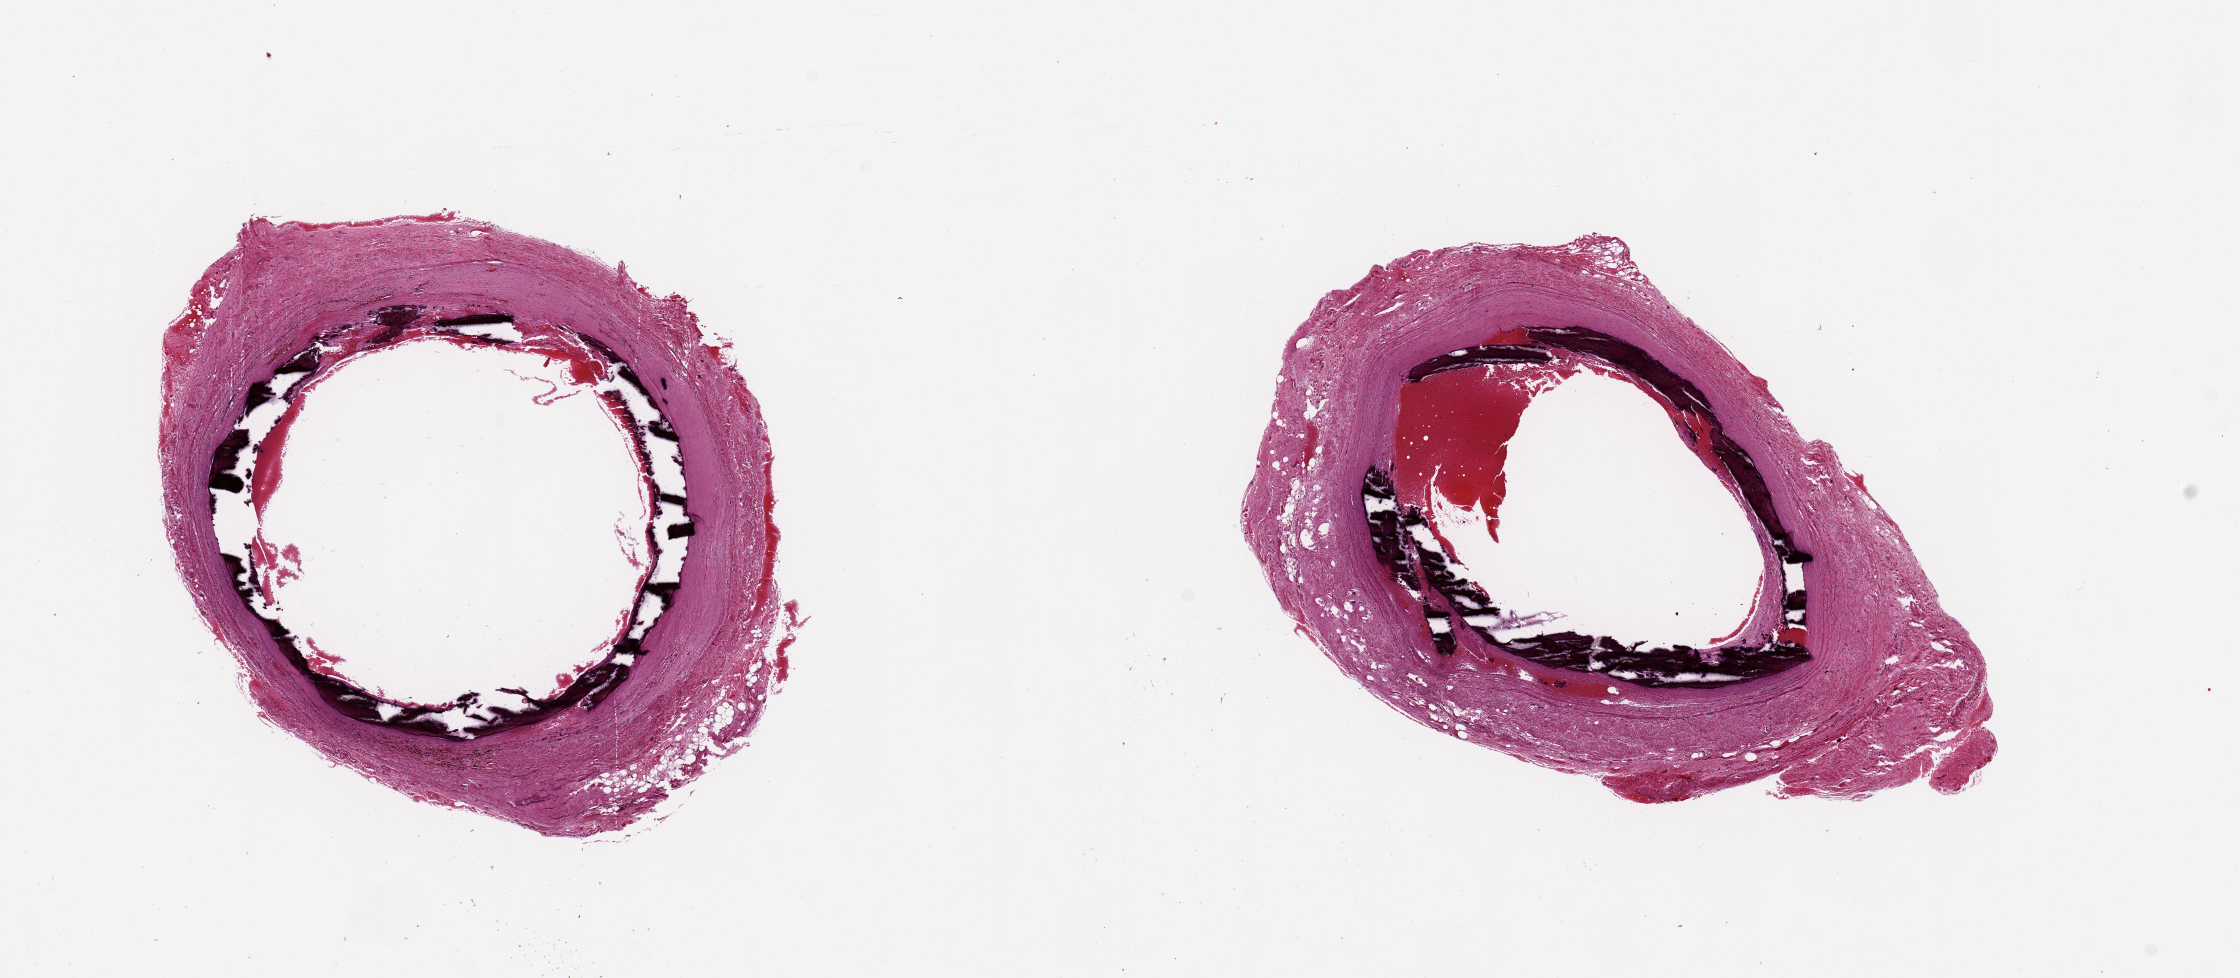
H&E whole-slide image — a low-resolution overview of the entire scanned area, about 17.7 x 7.7 mm (slide scanned at 20x). PAXgene-fixed paraffin-embedded (PFPE) section. Target tissue: coronary artery. Tissue donor sample. Donor sex: female.
Reviewer comment on this tissue sample: 2 ~5.5xmm aliquots, 20% circumferential calcified atherosclerotic luminal occlusion, ? hemorrhagic dissection.